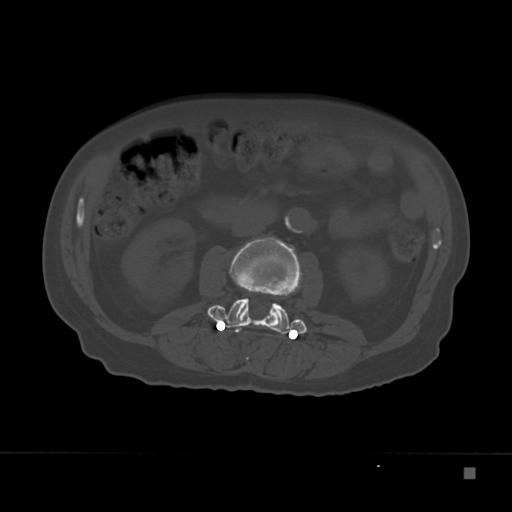
CT including the spine, one axial slice. 120 kVp. Bone window (W 1800 / L 400 HU). 1.5 mm slice thickness. 512 × 512 image matrix. Male patient, age 72 years. Case-level facts recorded for this patient, not image findings: primary cancer: skeletal.
Outlined on this slice (semi-automatically segmented with operator editing):
- L2 vertebra: bounding box <229,237,302,327> (left, top, right, bottom; pixels)
- L3 vertebra: <207,281,307,334>